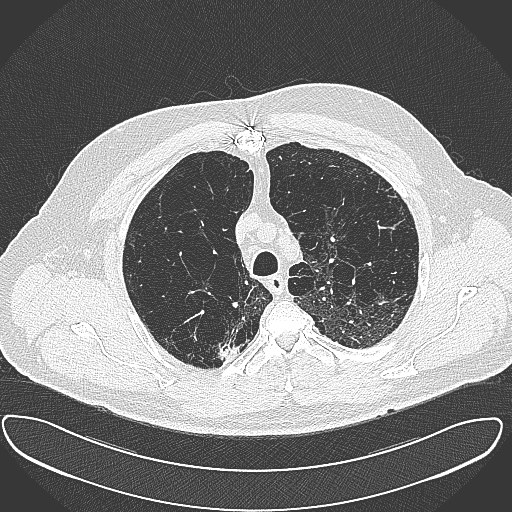
Chest CT (low-dose screening protocol), one axial image. First (baseline) screen. Lung window (W 1500 / L -600 HU). Lung (sharp) reconstruction kernel (B80f). Slice 80 of 385 in the series. Male participant, aged 60 years at enrolment. Current smoker at enrolment.
- Expert-annotated lung lesion, box from (x=202, y=328) to (x=241, y=363) px.
- Screening reader's record for this exam (one nodule recorded; not confirmed to be the boxed lesion): non-calcified nodule or mass ≥4 mm, right upper lobe, 15 × 25 mm, spiculated (stellate) margins, soft tissue attenuation.
- Lung cancer was diagnosed 32 days after this screen: carcinoma, NOS, right upper lobe, moderately differentiated (G2), stage IB (AJCC 6th edition), 35 mm at pathology.